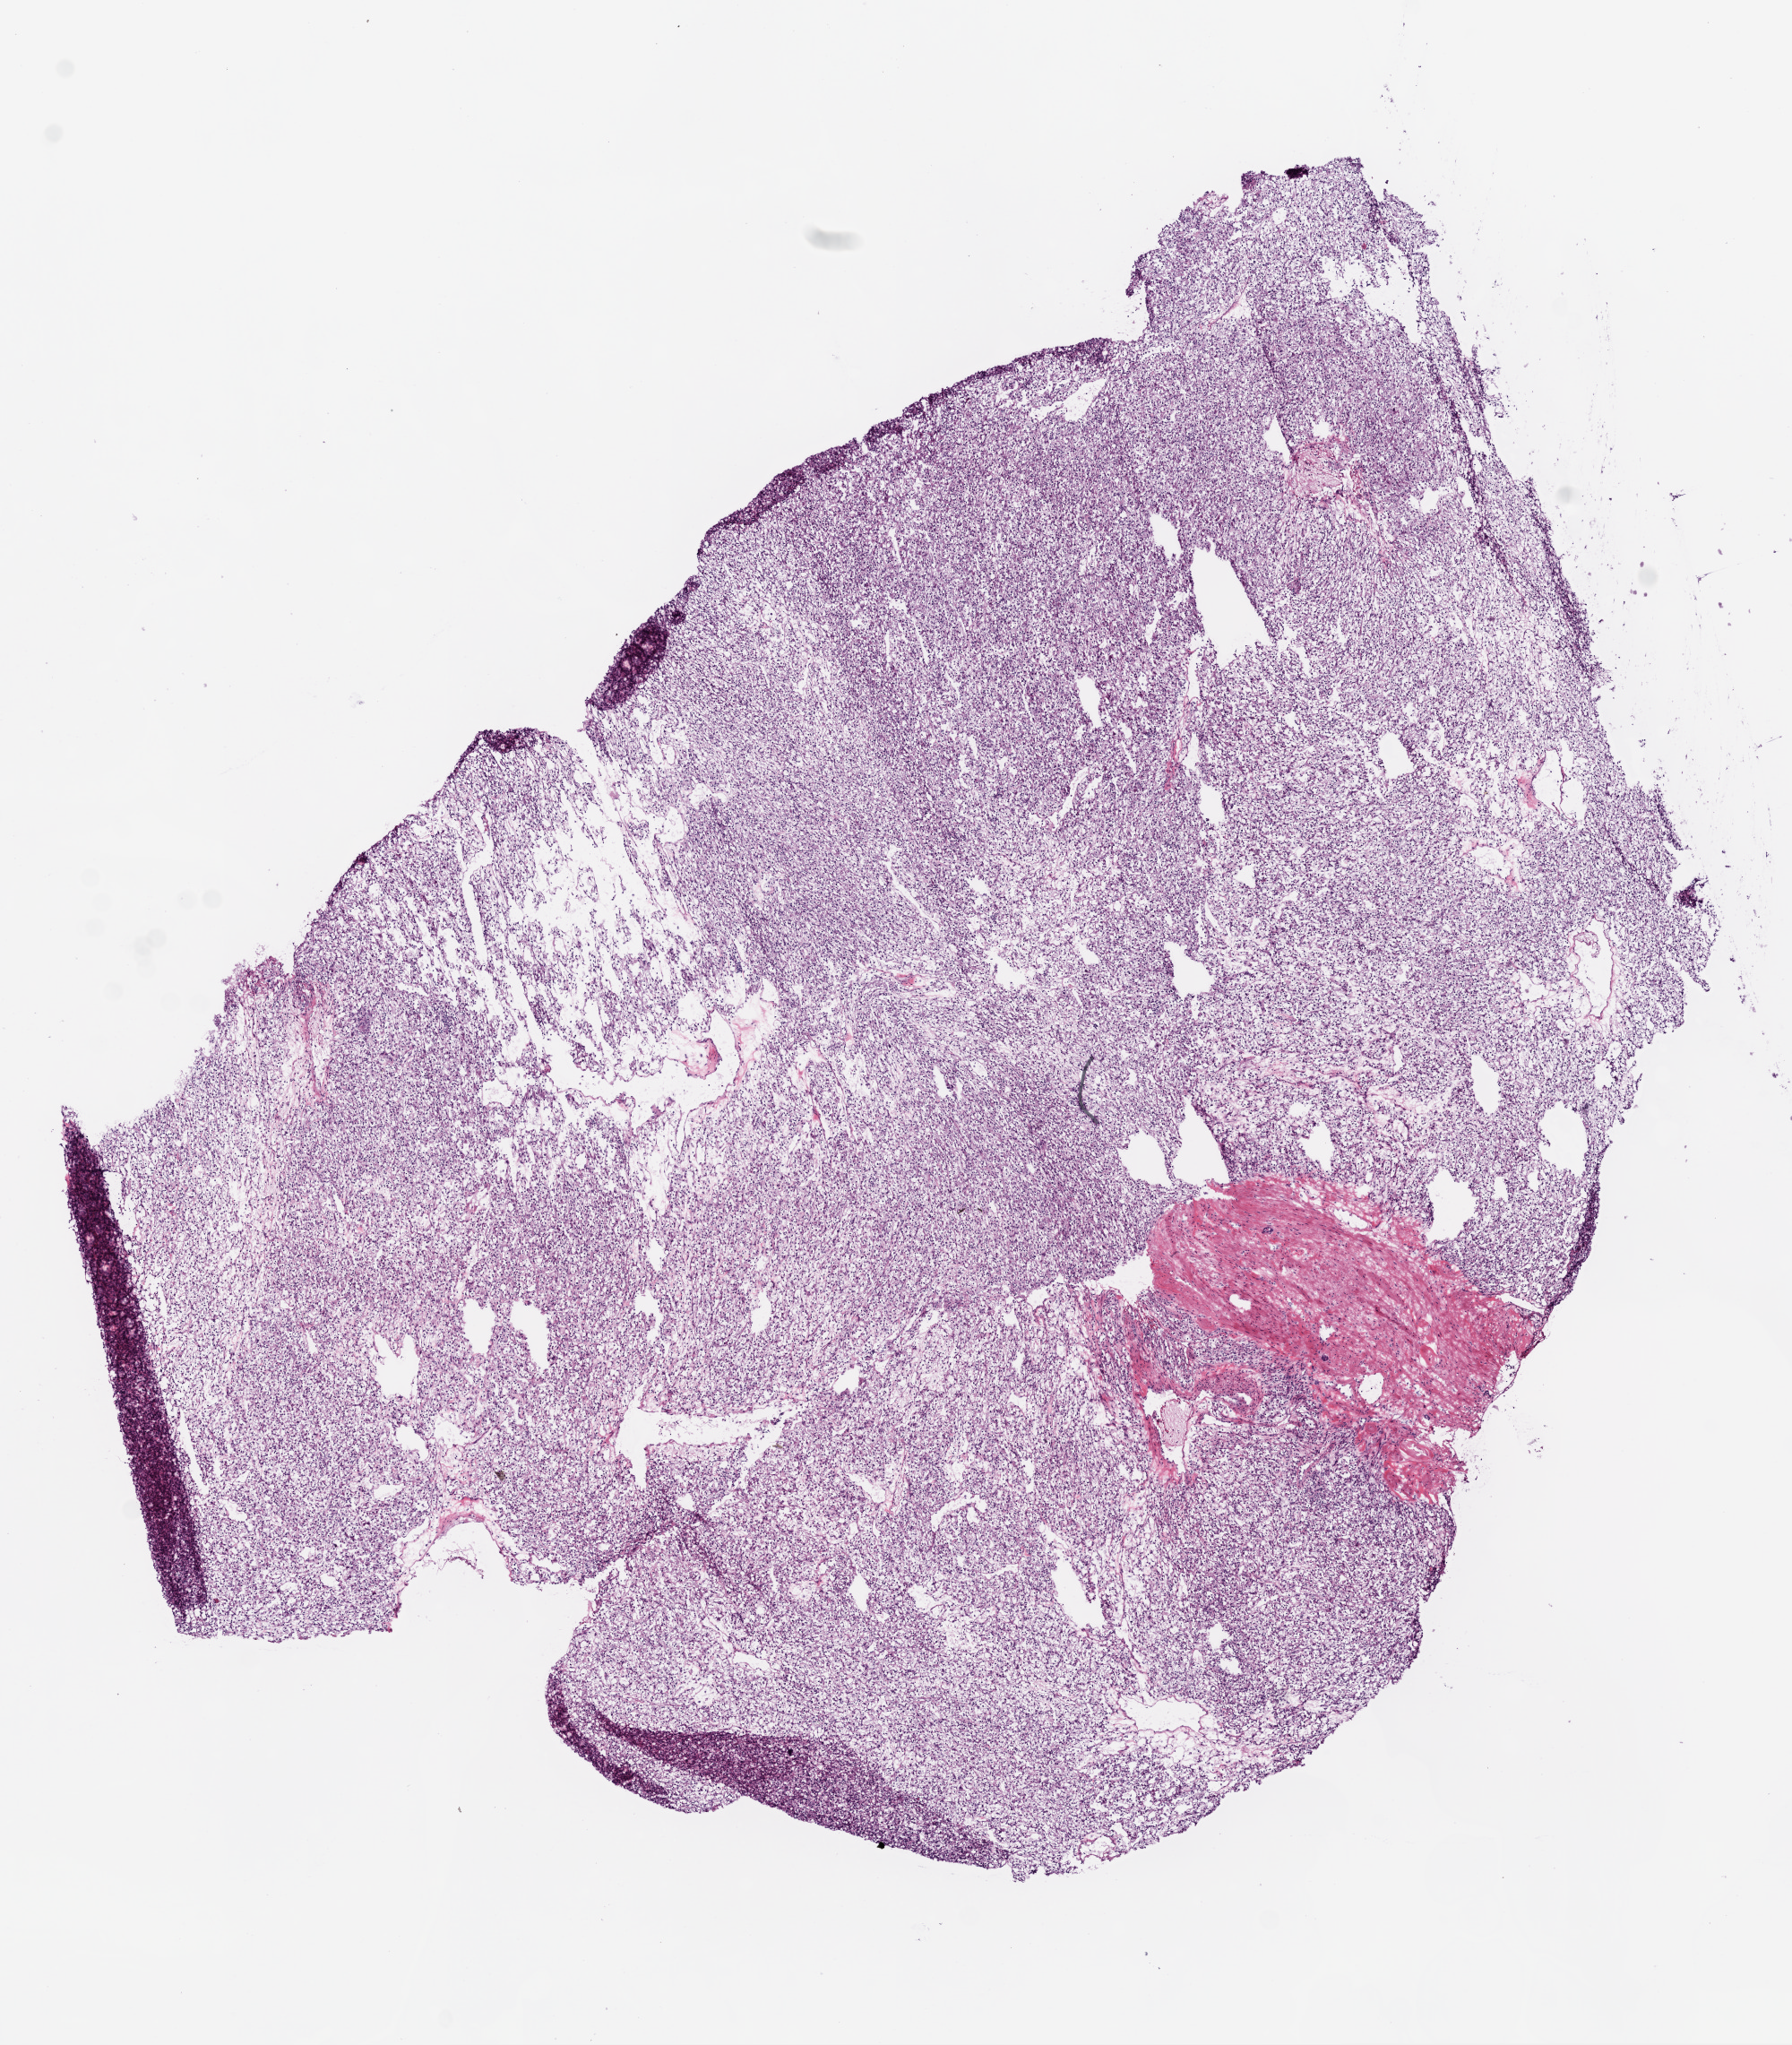
Digitized Hematoxylin and eosin (H&E) stained tissue section (whole slide) — a low-resolution overview of the entire scanned area, about 8.0 x 9.2 mm (acquisition: 20x scan). Frozen section. Primary tumour sample from the kidney. Patient: male, age at initial diagnosis 66 years. Histologic grade: G3 (poorly differentiated). Pathologist review of this section (percent, as recorded): tumour cells 90%, tumour nuclei 90%, normal cells 5%, stromal cells 5%, necrosis 0%.
AJCC pathologic stage: III. Diagnosis: Clear cell adenocarcinoma, NOS.